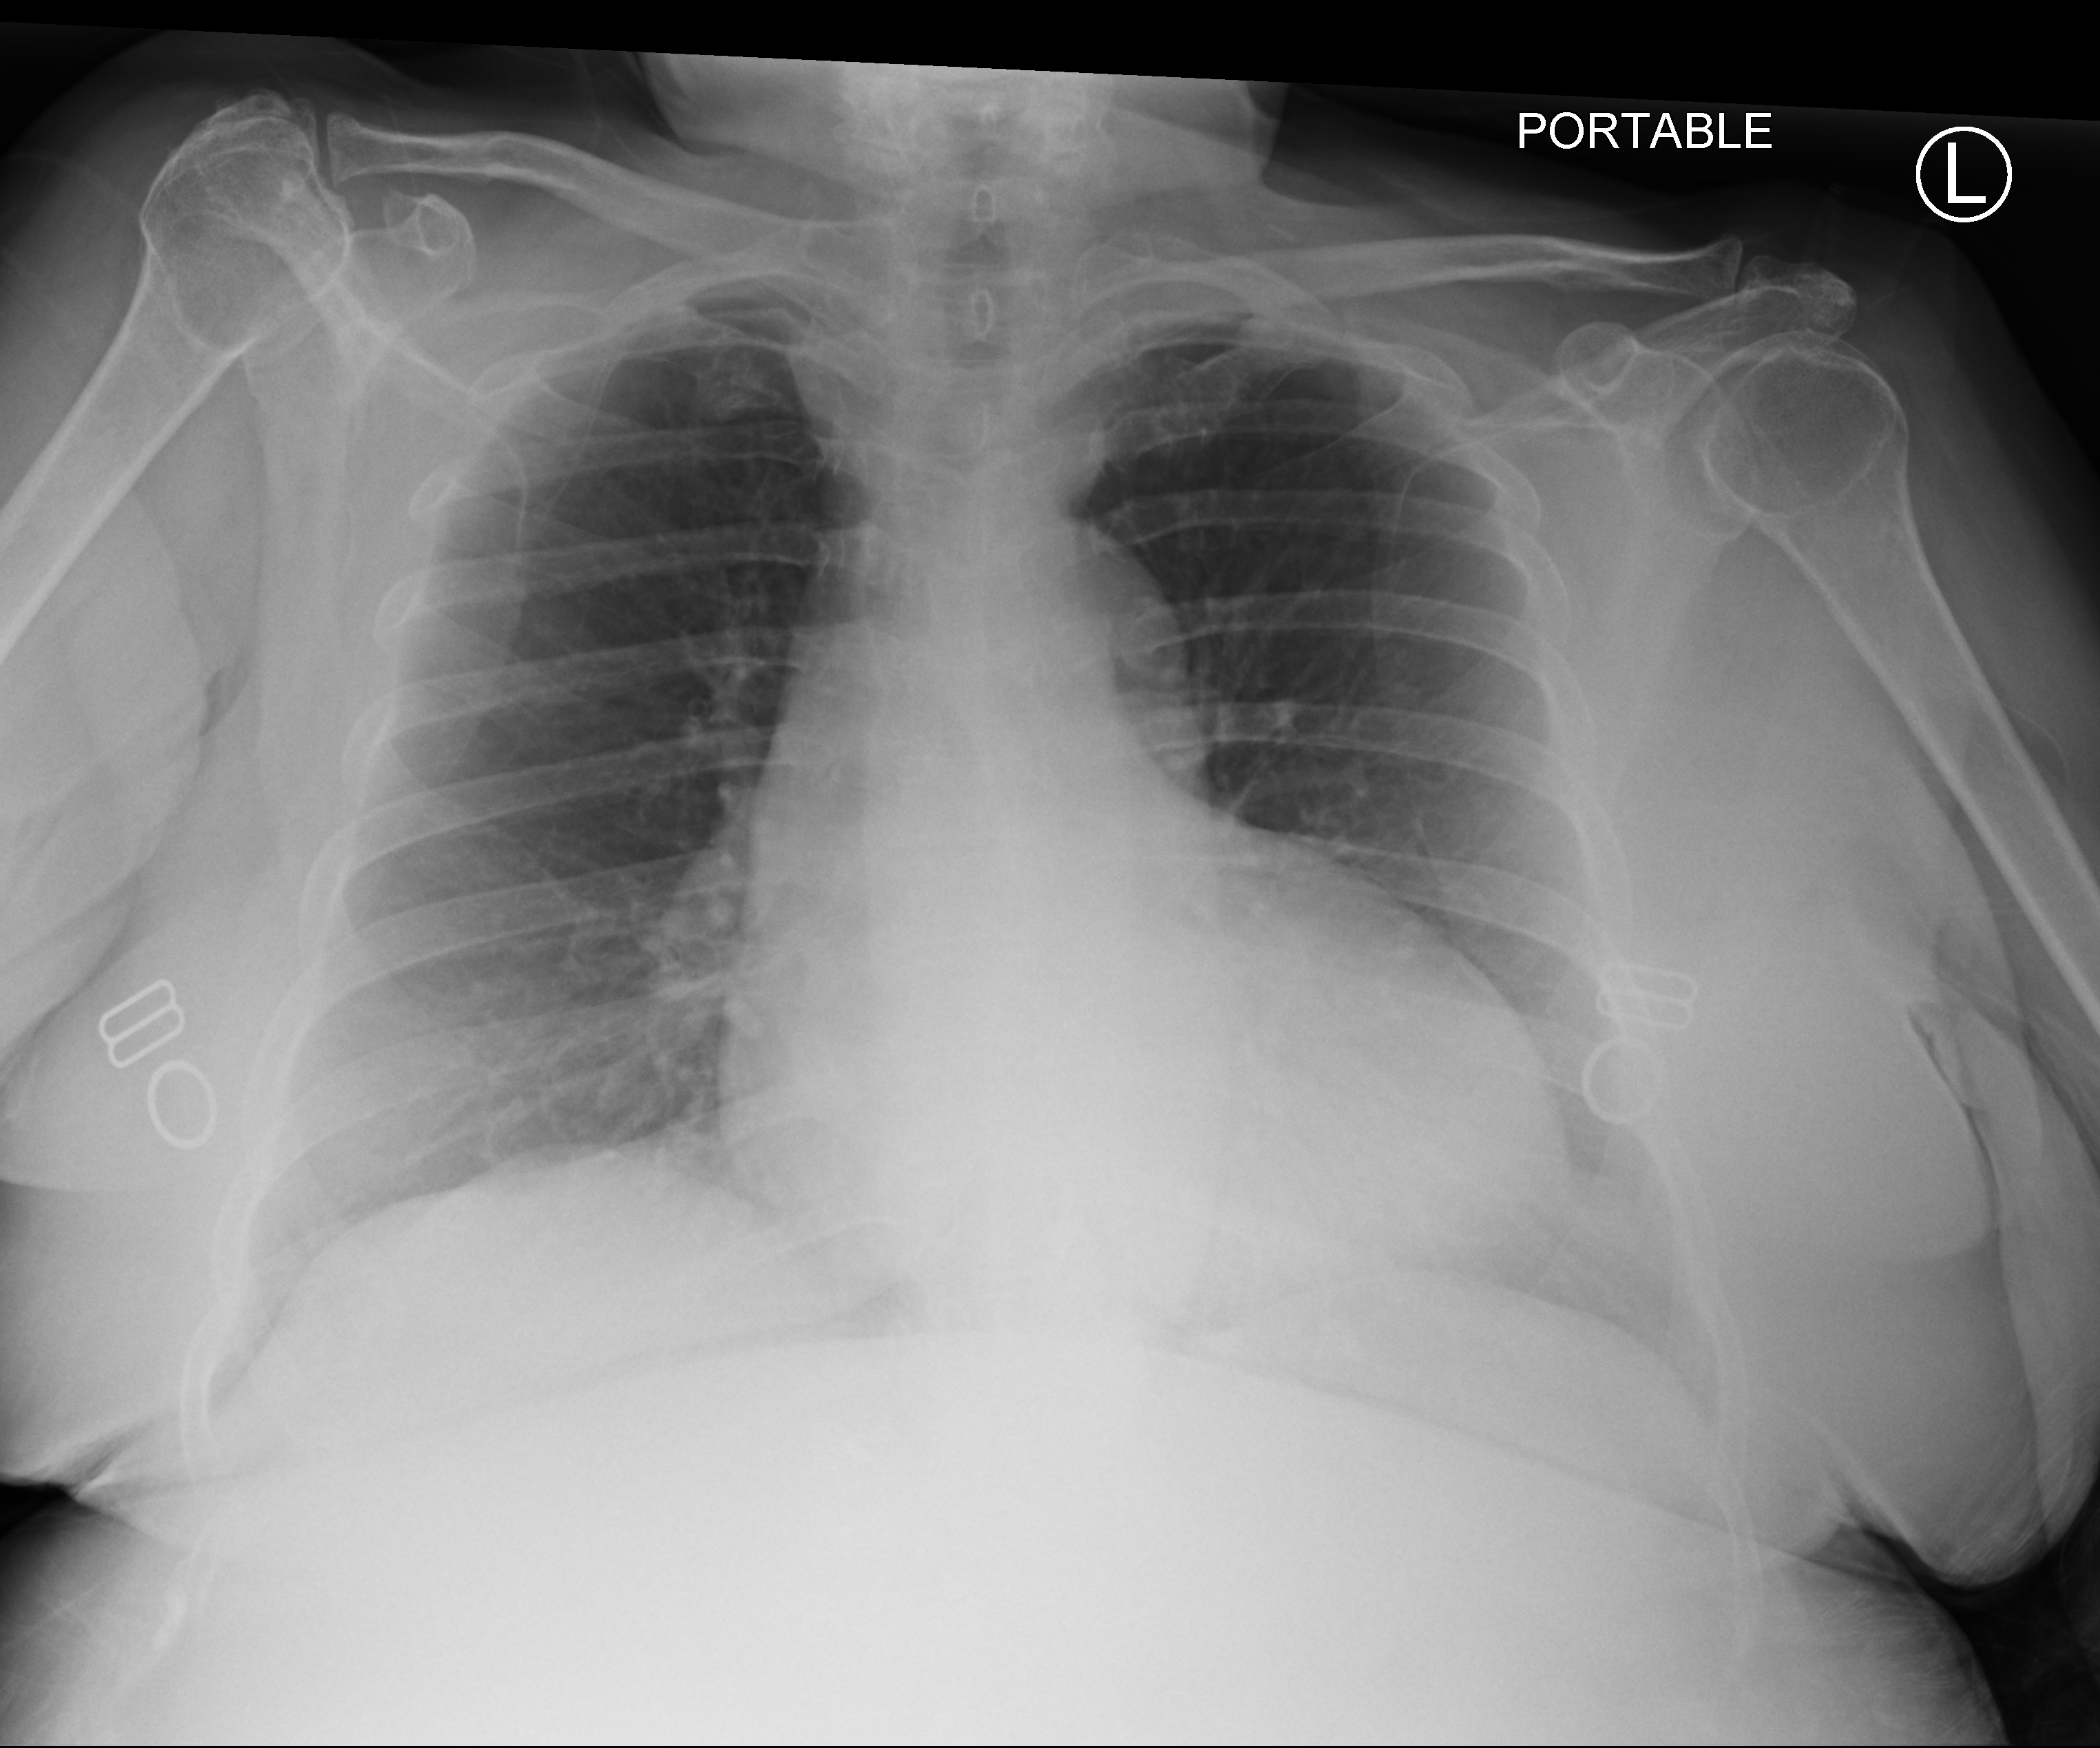
Portable chest radiograph, anteroposterior (AP) projection. Female patient hospitalised with COVID-19, age 75–90 years.
Admission-level facts for this patient (not findings on this image; timing relative to this image not recorded): length of hospital stay: 1 day; admitted to intensive care during this hospital stay: no; mechanically ventilated during this hospital stay: no.